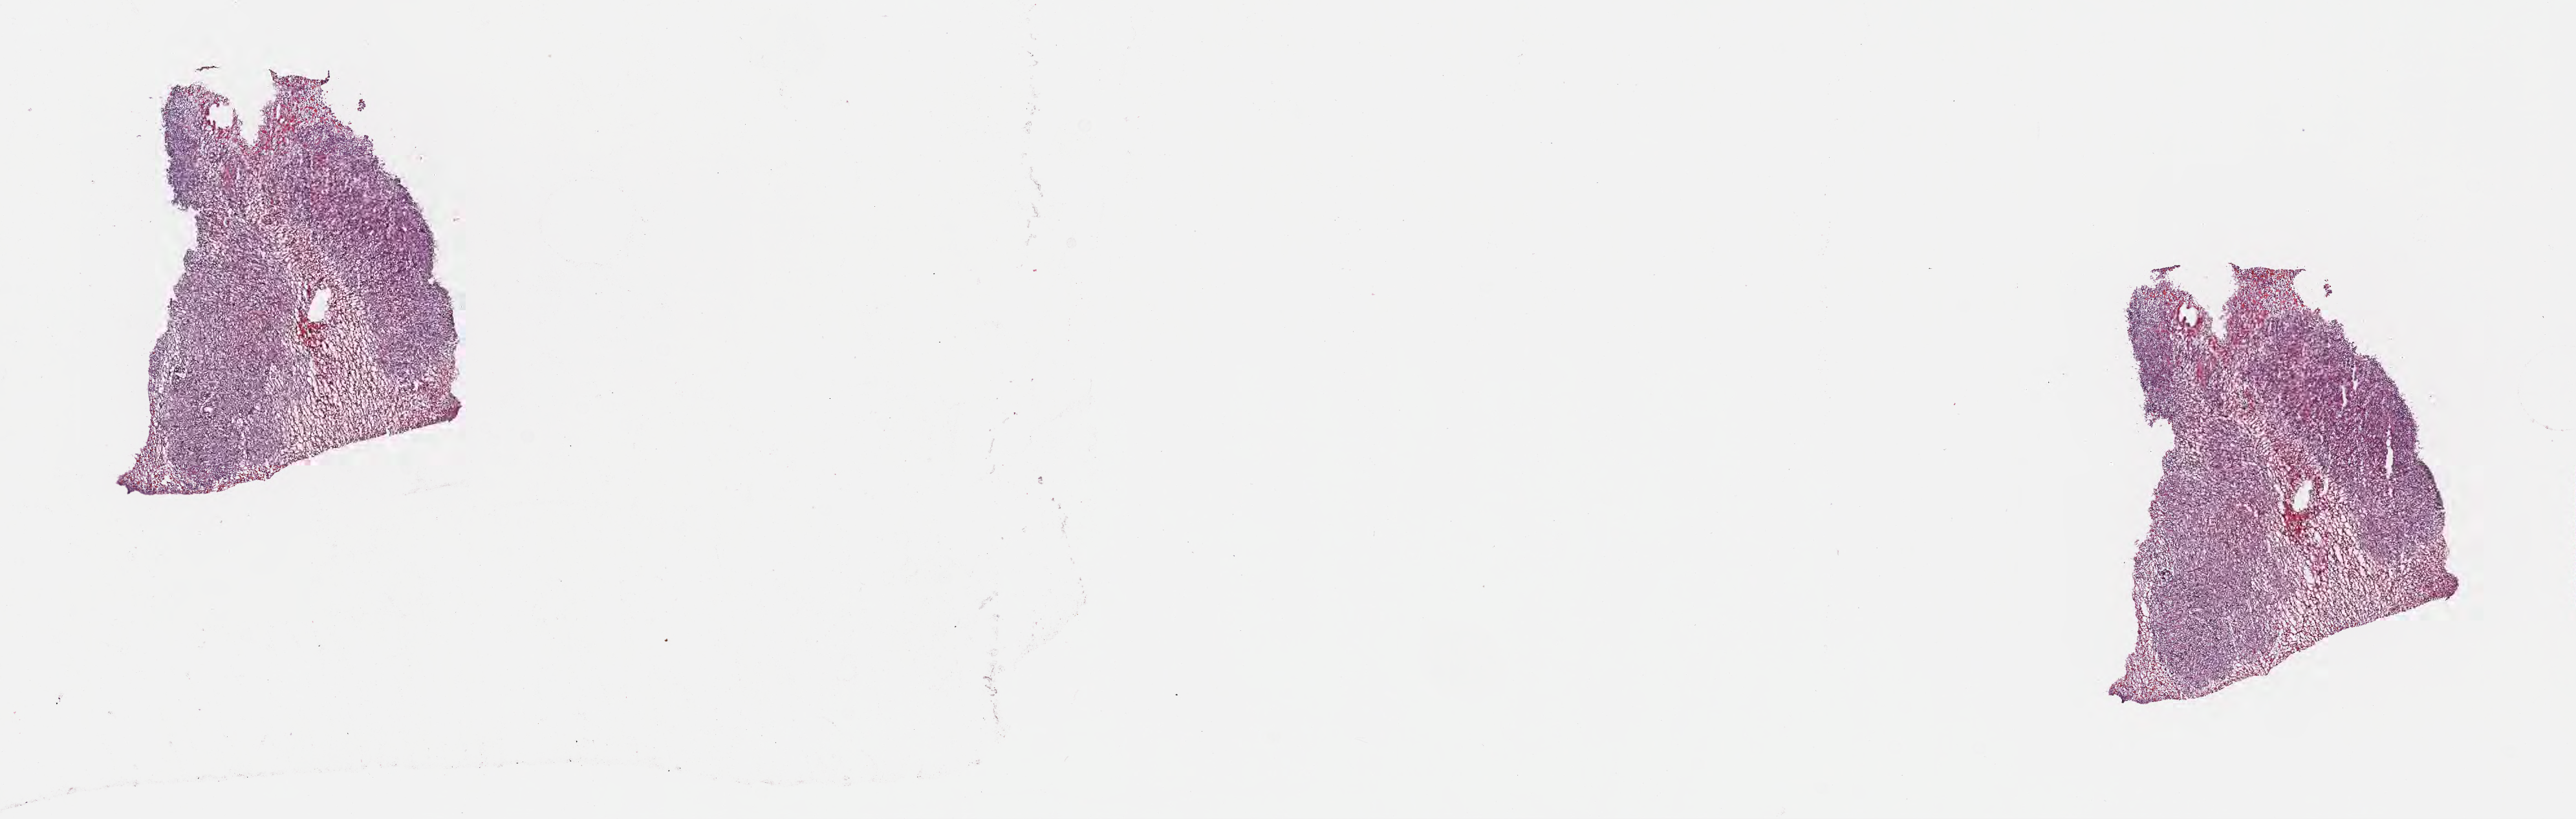
Digitized H&E-stained section — whole scanned area (about 16.1 x 5.1 mm) shown as a low-resolution overview, frozen section, primary tumor. Patient: female, age at initial diagnosis 8 years. Pathologist review of this section (percent, as recorded): tumor cells 65%, tumor nuclei 75%, stromal cells 30%, necrosis 5%, normal cells 0%. Infiltration values recorded for this section: lymphocyte infiltration 60%, monocyte infiltration 20%, neutrophil infiltration 5%.
• diagnosis: Burkitt lymphoma, NOS